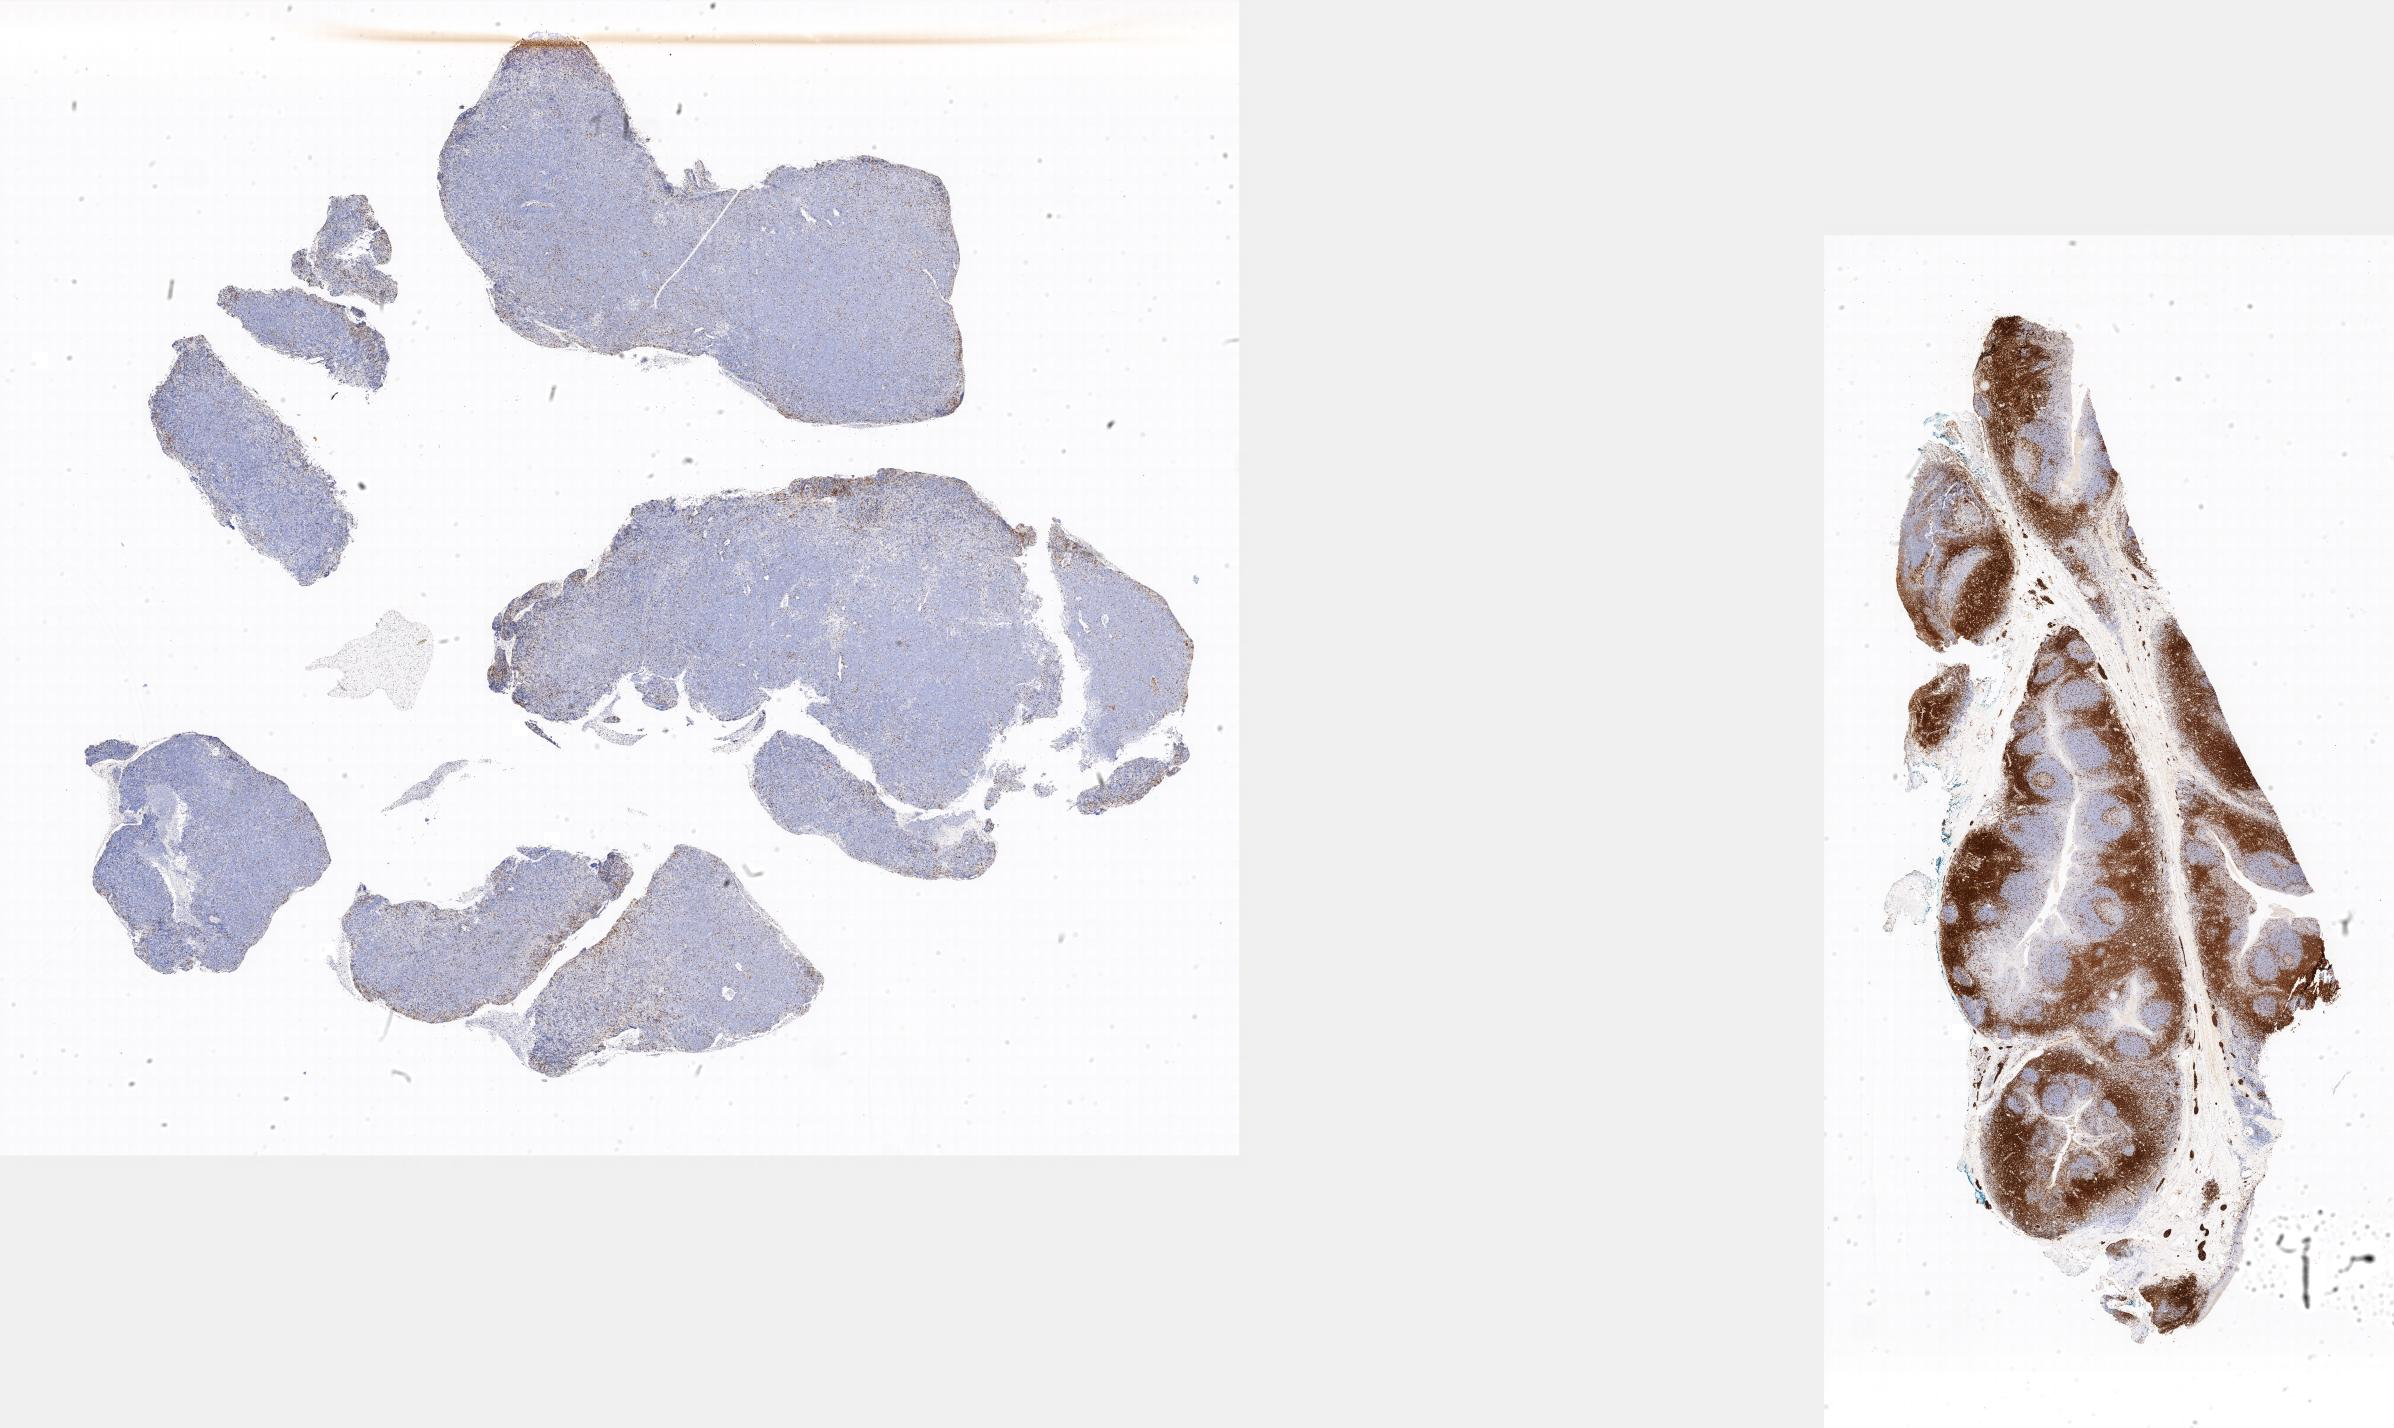
IHC for CD3, whole-slide image, low-resolution overview of the scanned area; tumor tissue; anatomic site: soft tissue. Female patient; age at initial diagnosis 9 years.
- diagnosis: Burkitt lymphoma, NOS